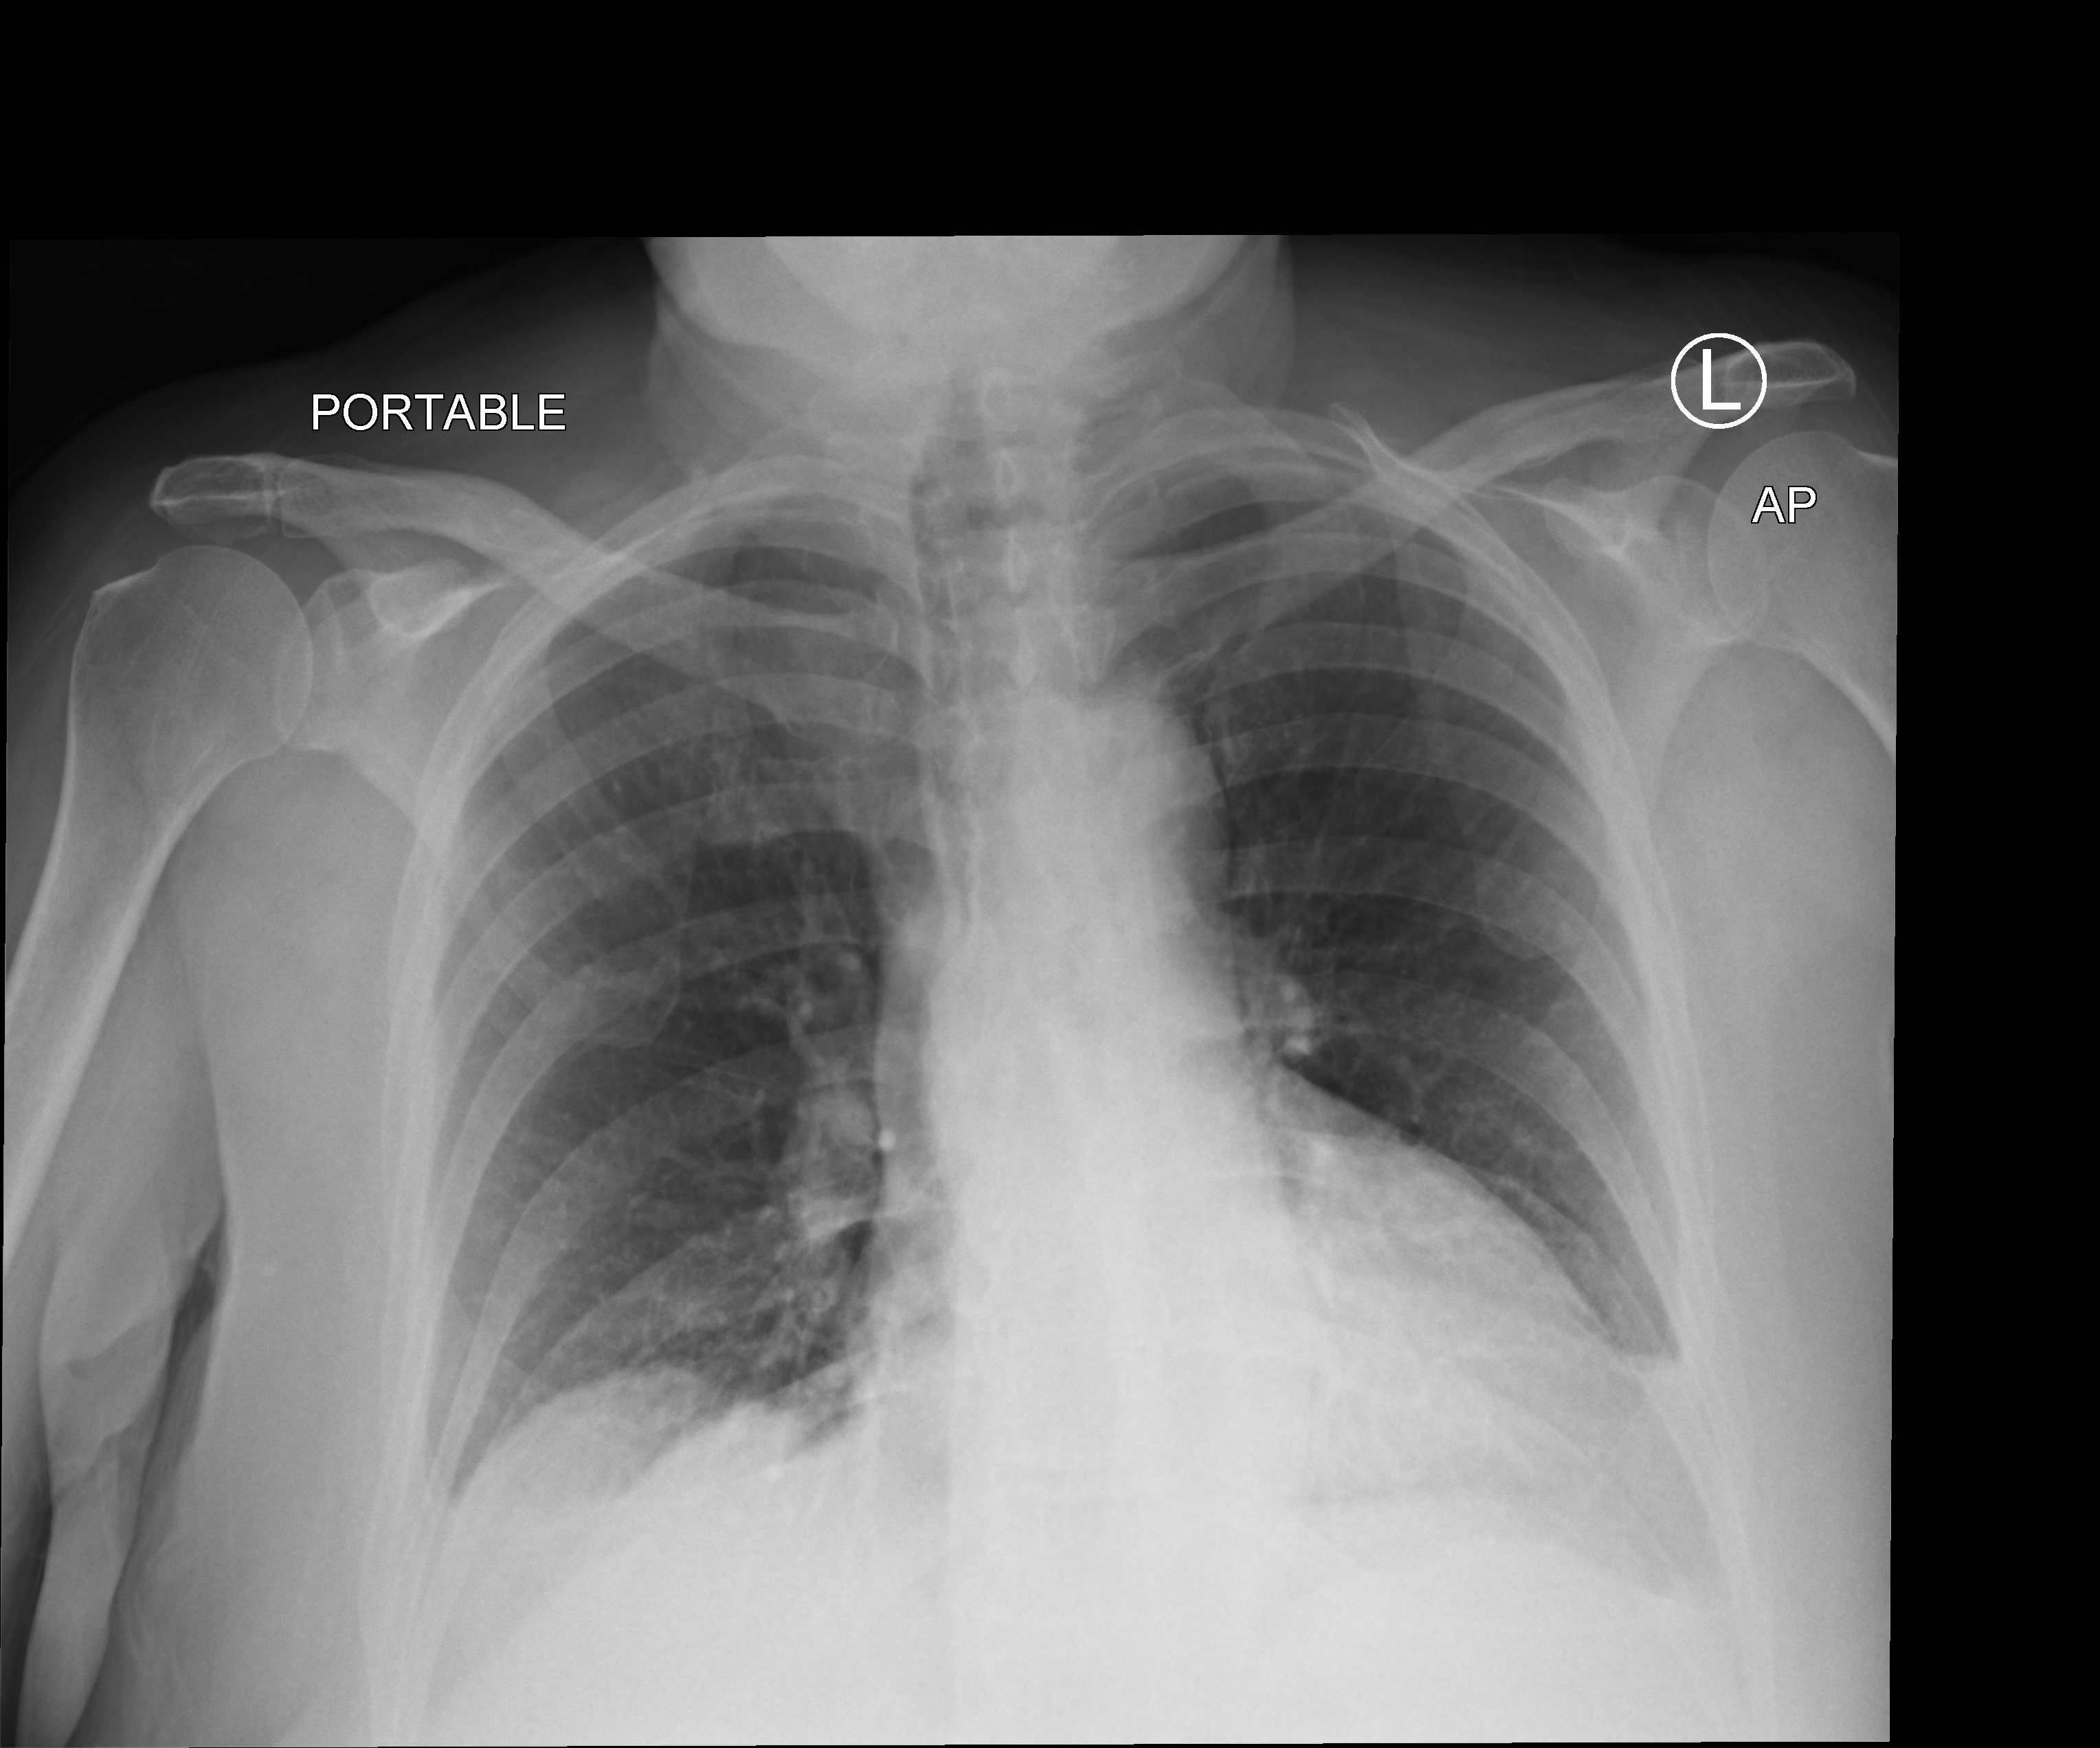
Chest X-ray (portable). Female patient hospitalised with COVID-19, age 75–90 years.
Admission-level facts for this patient (not findings on this image; timing relative to this image not recorded): admitted to intensive care during this hospital stay: no; mechanically ventilated during this hospital stay: no.